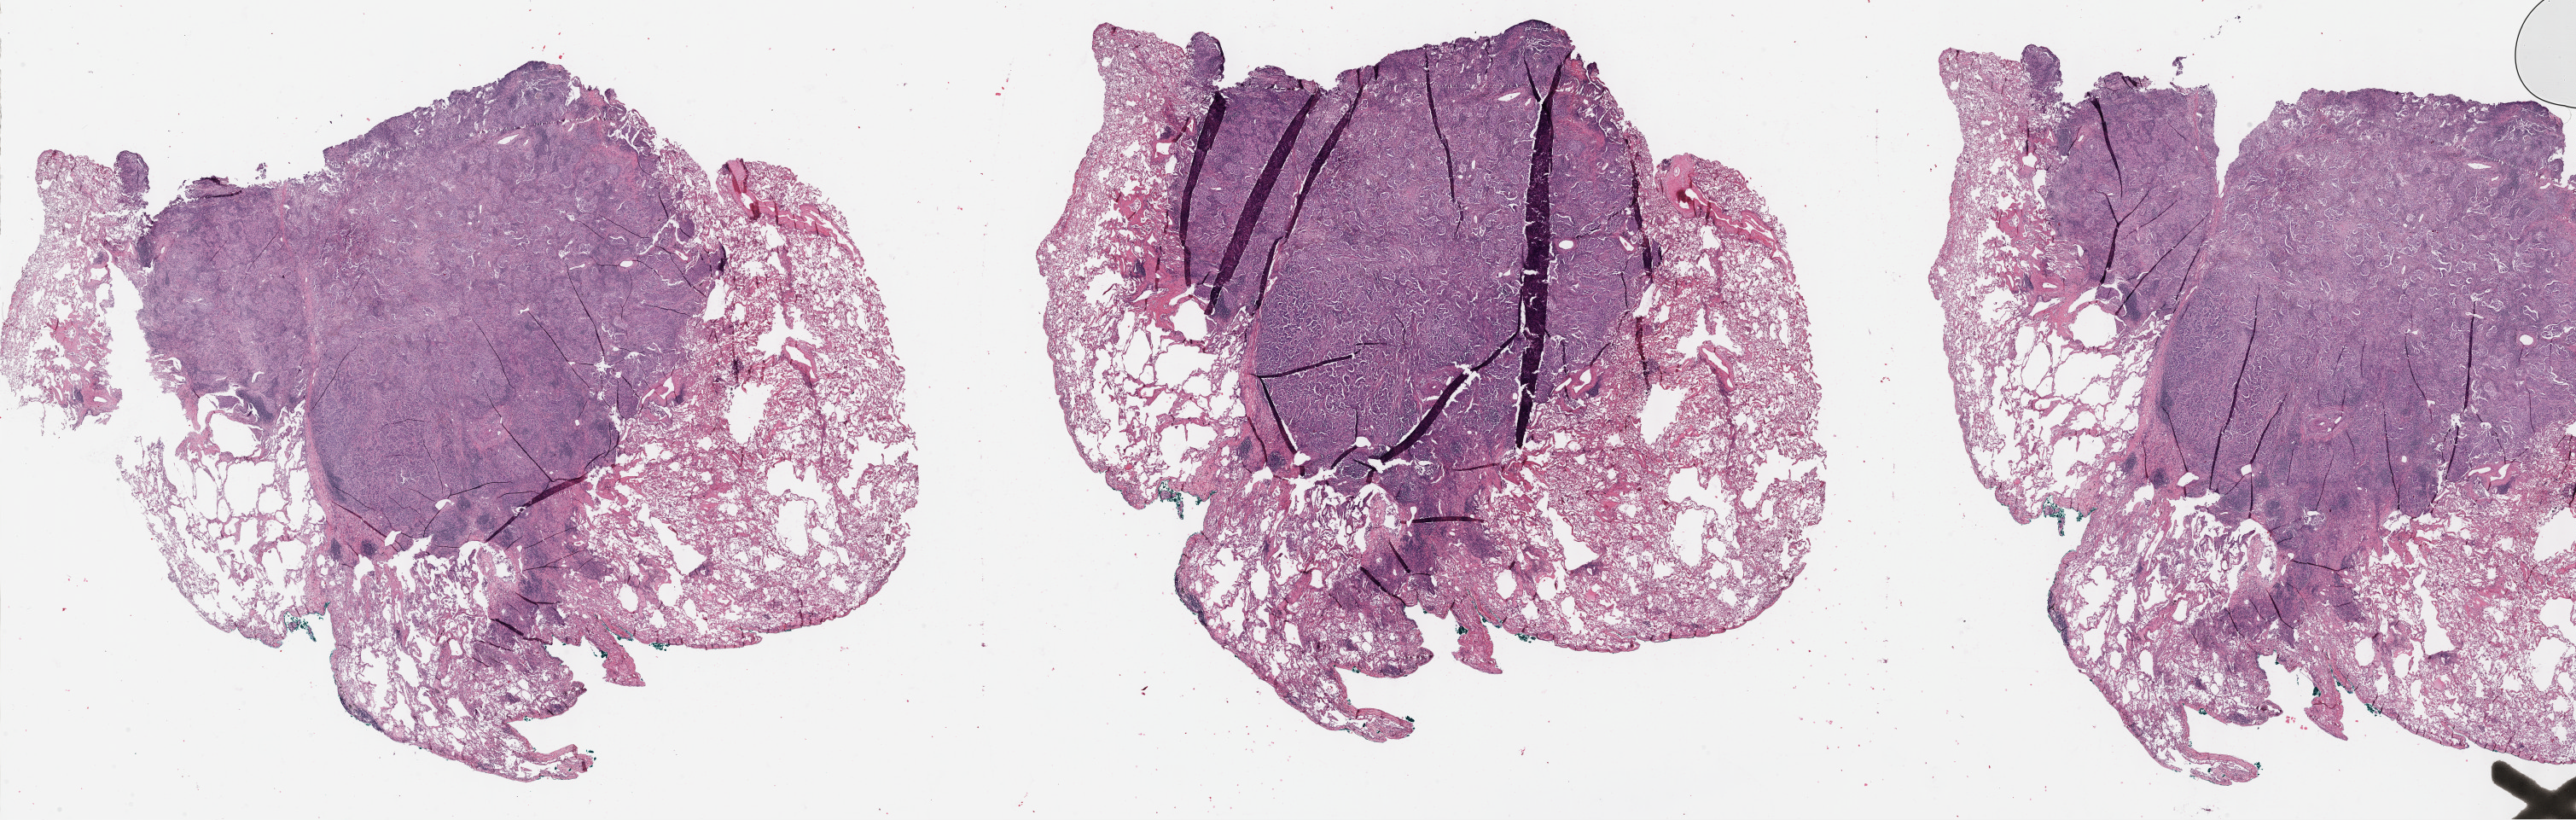
Whole-slide histology image, Hematoxylin and eosin (H&E) stained, a low-resolution overview of the entire scanned area, about 48.8 x 15.5 mm. Formalin-fixed paraffin-embedded (FFPE) diagnostic section. Lung, primary tumour sample. Female patient; age at initial diagnosis 69 years.
• laterality: left
• AJCC pathologic stage: IA (7th edition)
• histologic diagnosis: Adenocarcinoma with mixed subtypes